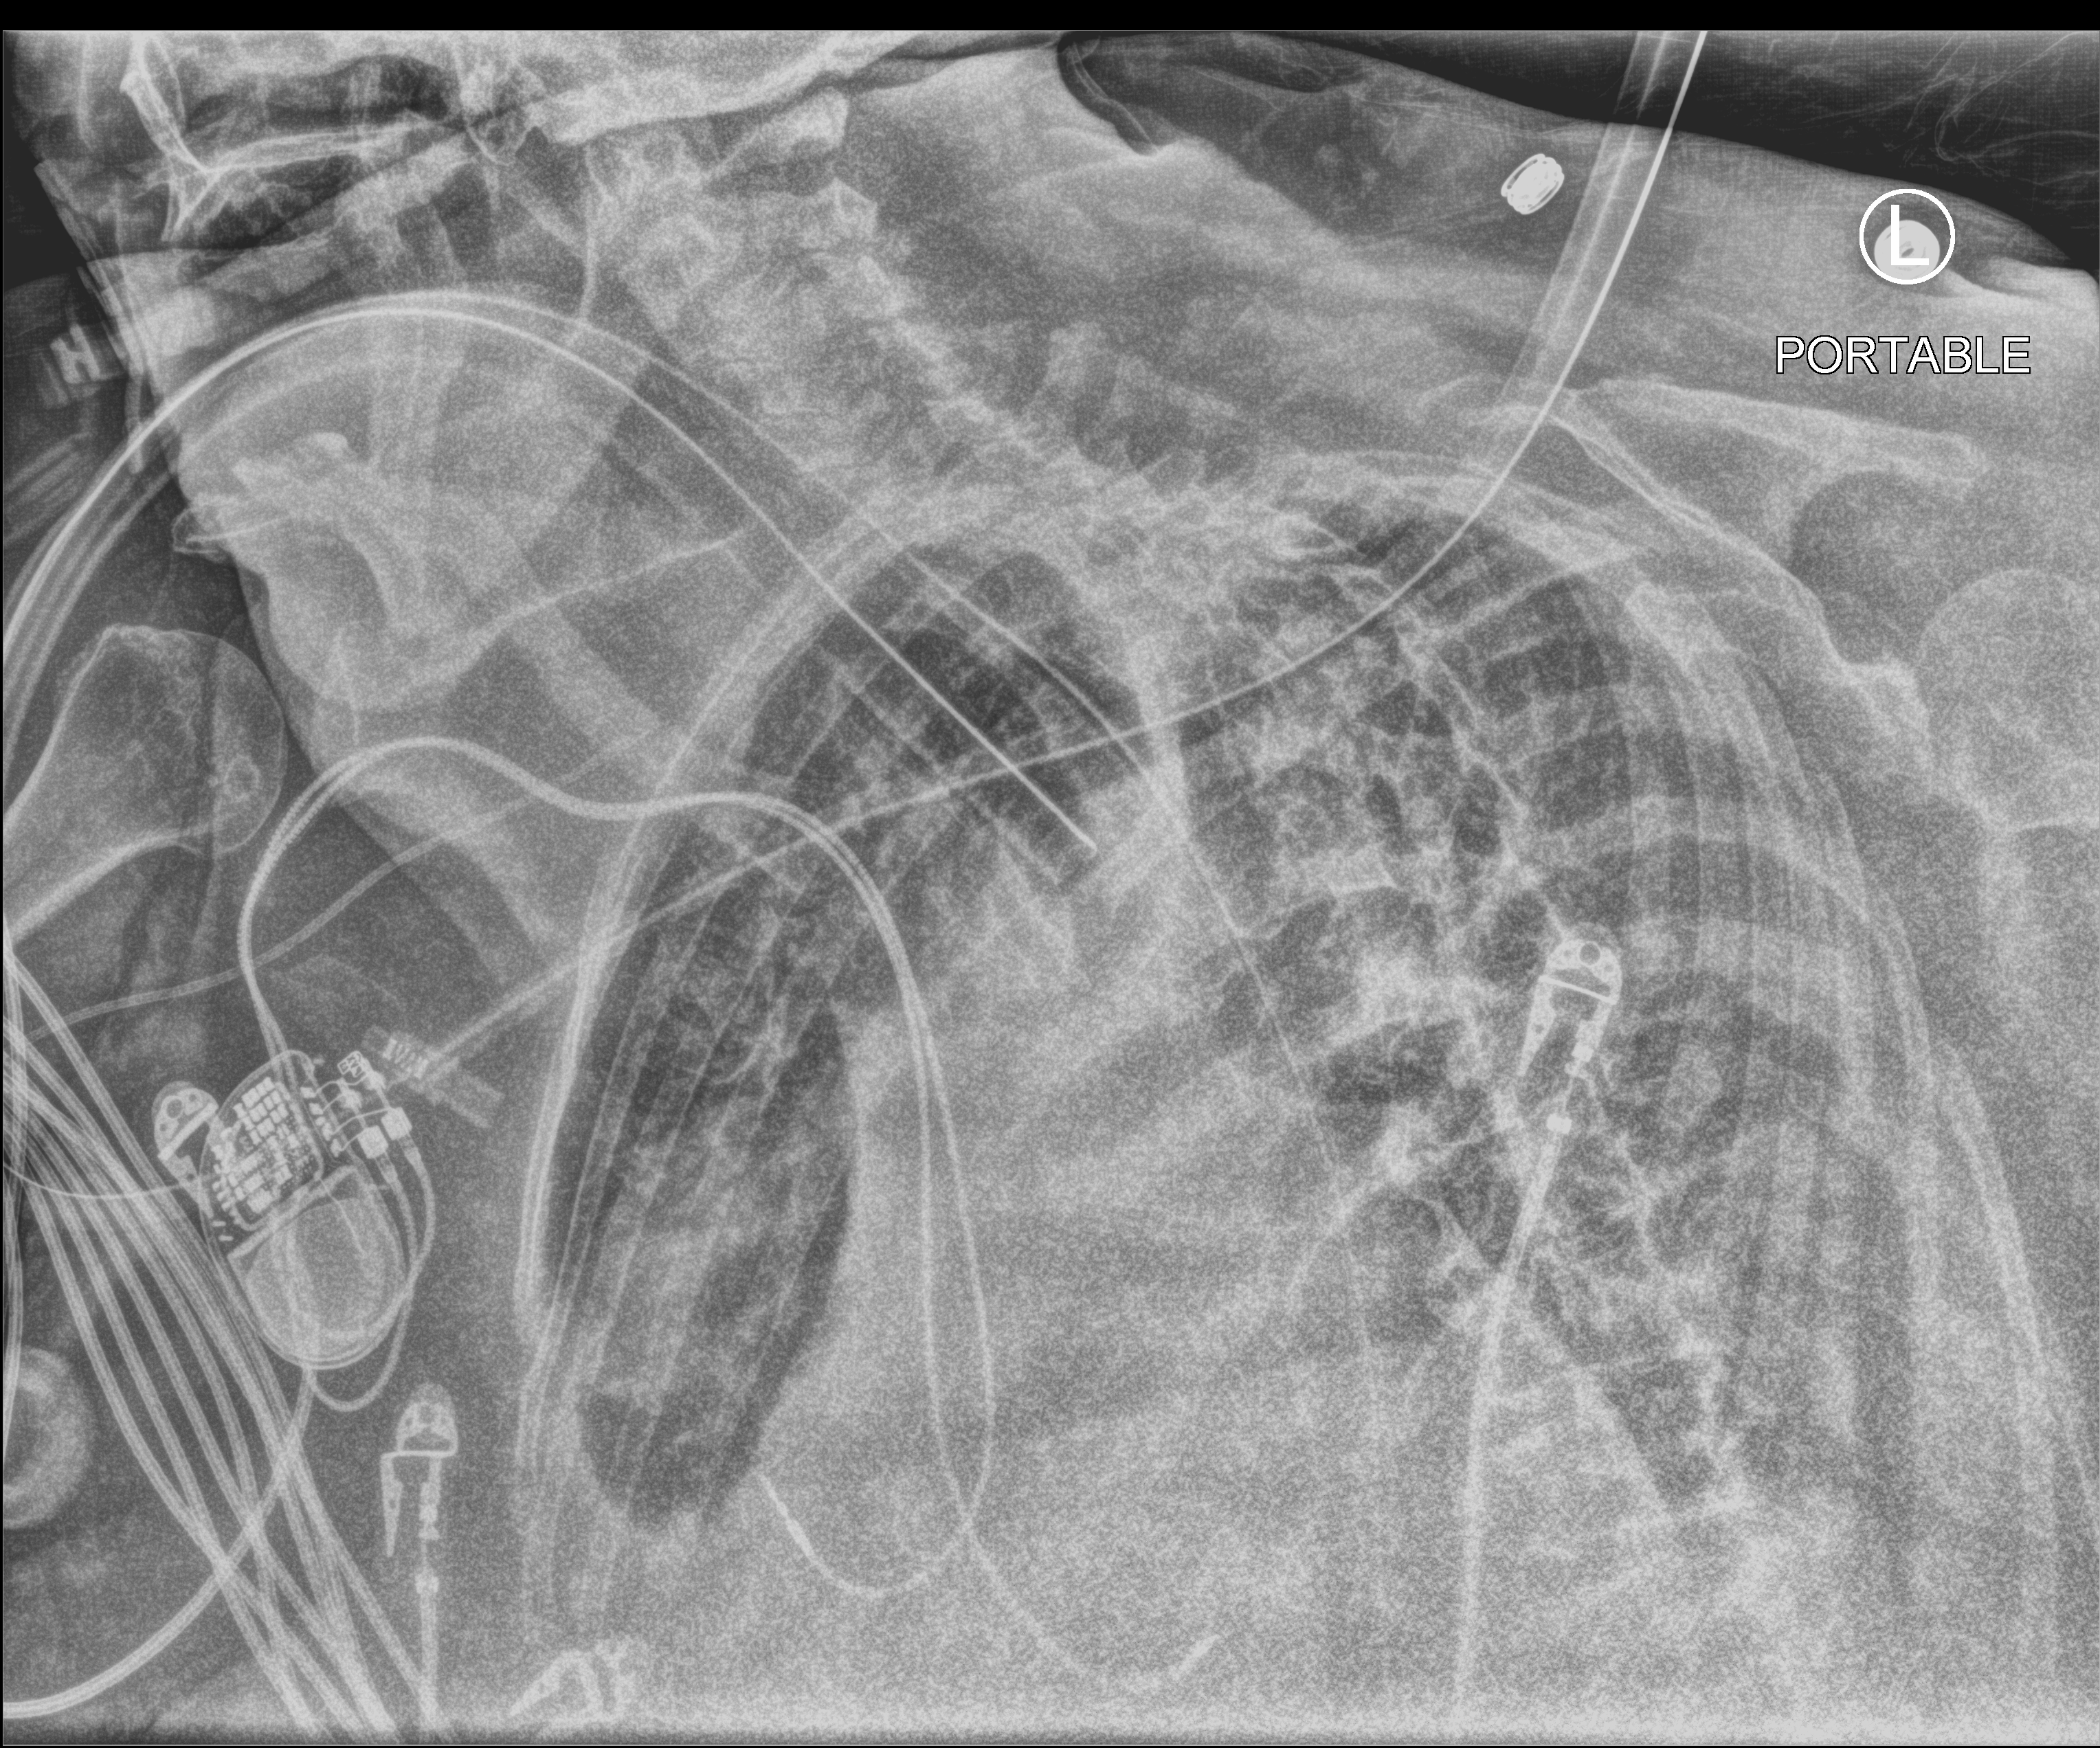
Portable chest radiograph; anteroposterior (AP) projection. Patient hospitalised with COVID-19; female, aged 75–90 years.
Admission-level facts for this patient (not findings on this image; timing relative to this image not recorded): hypertension (admission record): yes; admitted to intensive care during this hospital stay: yes.